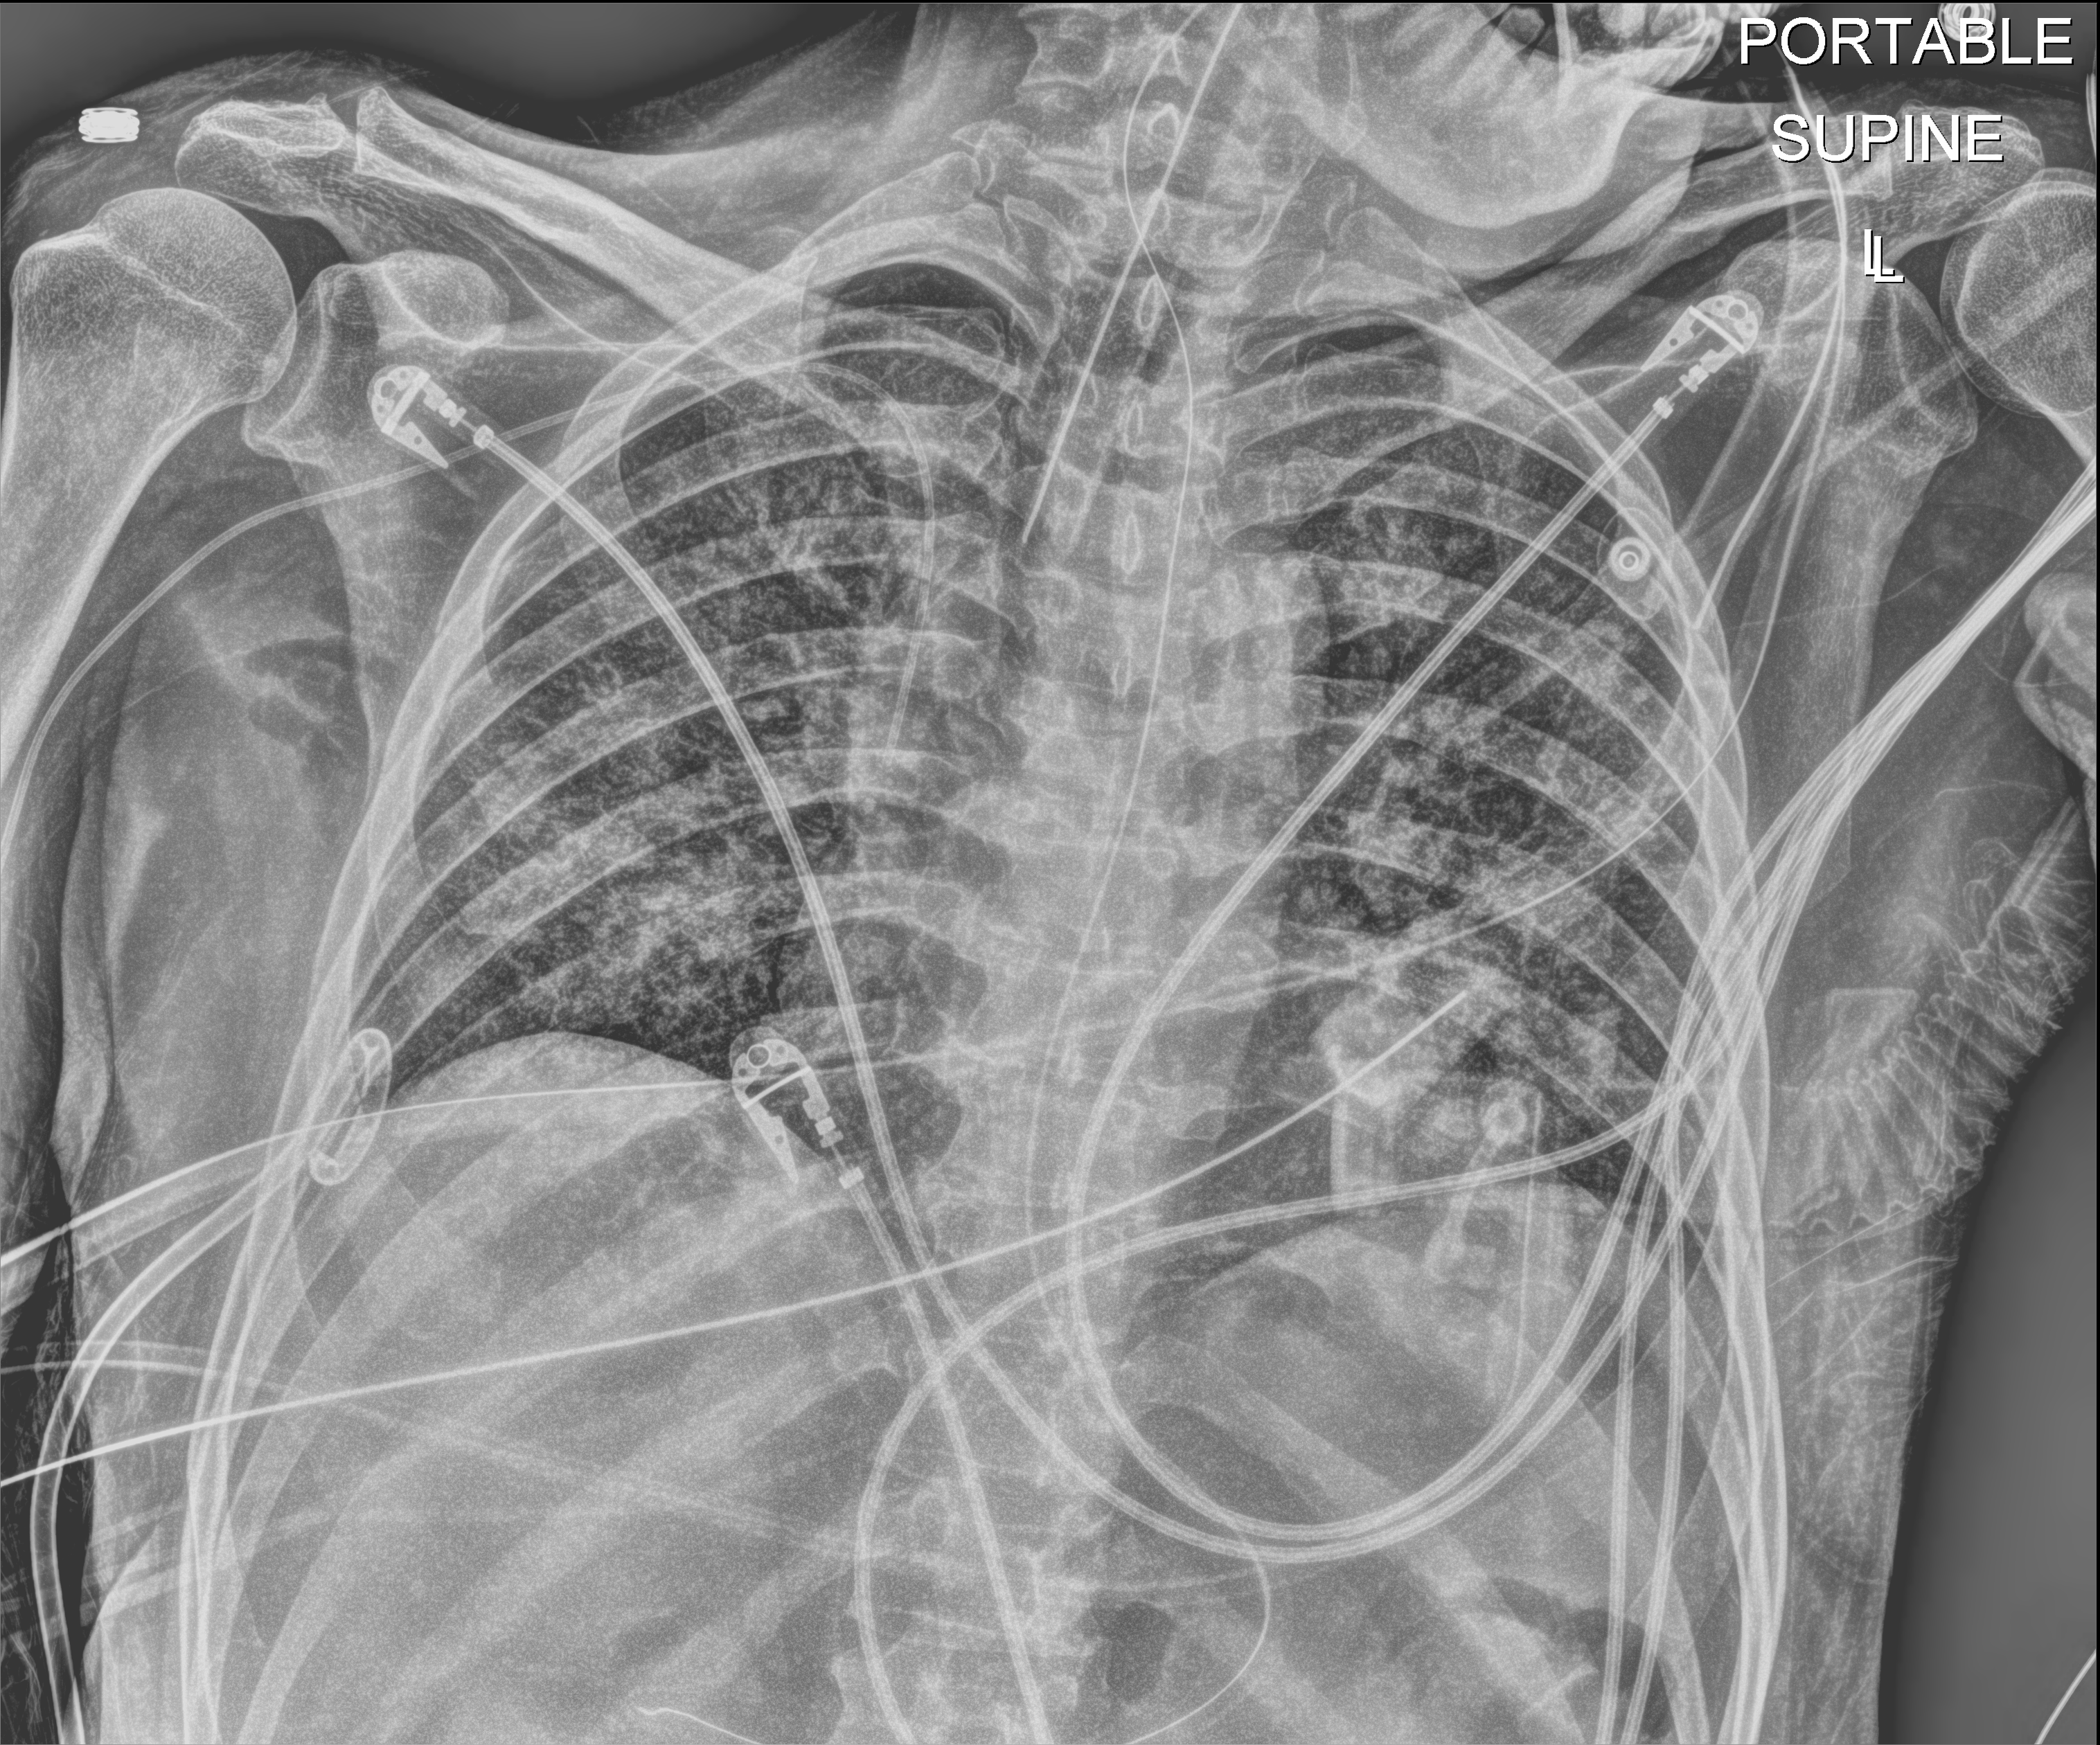
Bedside chest radiograph (digital radiography), anteroposterior (AP) projection. Male patient hospitalised with COVID-19, age 18–59 years.
From the hospital-stay record, not from the radiograph (when in the stay this image was taken is not recorded): length of hospital stay: 77 days; smoking status (admission record): never.